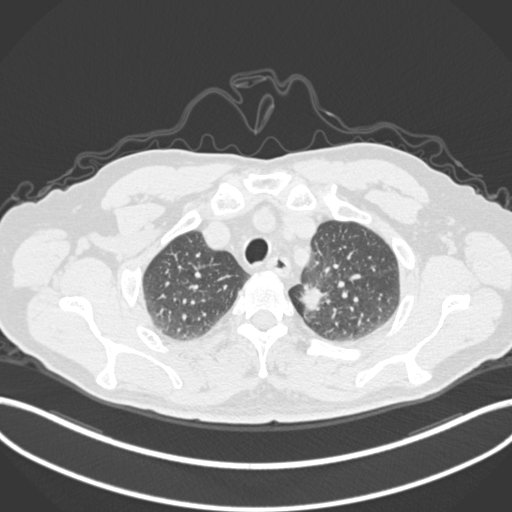
Chest CT, one axial slice; position 270 of 306 along the scan axis; reconstruction kernel B30f; lung window (W 1500 / L -600 HU); 512 × 512 image matrix, field of view 400 × 400 mm. Patient: male, 64 years. Case-level facts recorded for this patient, not image findings: clinical TNM (as recorded): T1c N0 M0.
Outlined on this slice (rectangle marked by the reading radiologist):
- lung tumour (recorded histology: adenocarcinoma): bounding box <294,276,333,318> (left, top, right, bottom; pixels)